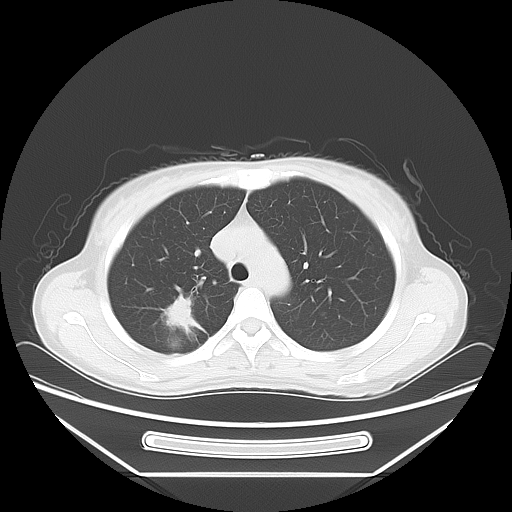
Chest CT, one axial slice; position 49 of 66 along the scan axis; reconstruction kernel LUNG; 120 kVp; lung window (W 1500 / L -600 HU); 512 × 512 image matrix, field of view 408 × 408 mm. Patient: female, 37 years. Case-level facts recorded for this patient, not image findings: clinical TNM (as recorded): T1c N0 M1.
Structures marked on this image (bounding box drawn by a radiologist):
- lung tumour (recorded histology: adenocarcinoma): bounding box <162,295,200,336> (left, top, right, bottom; pixels)